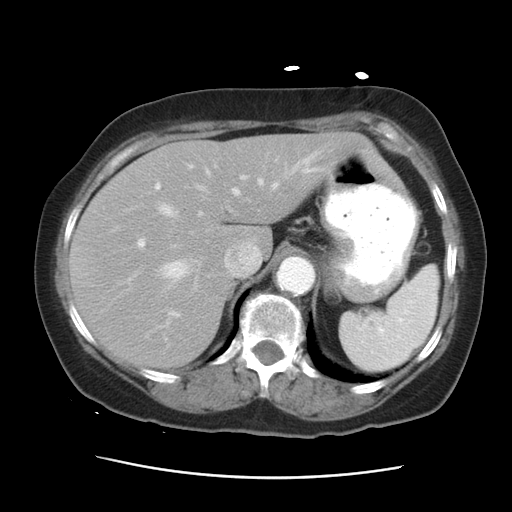
Contrast-enhanced abdominal CT, one axial slice. Slice 21 of 29 in the series (ordered by position). 120 kVp. Intravenous contrast given. Soft-tissue window (W 400 / L 40 HU). 512 × 512 image matrix, field of view 354 × 354 mm. Female patient, age 64 years. From the clinical record (not read from this slice): diagnosis: colorectal cancer liver metastases, imaged before liver resection; multiple liver metastases: no; largest metastasis: 2.5 cm; disease in both lobes: no.
Annotated regions visible in this slice (manually delineated by an expert):
- hepatic veins: bounding box (x1, y1, x2, y2) in pixels: (158, 151, 323, 328)
- liver: (70, 134, 371, 368)
- planned liver remnant (the part of the liver to remain after resection): (70, 134, 371, 285)
- portal vein (with intrahepatic branches): (137, 161, 201, 316)